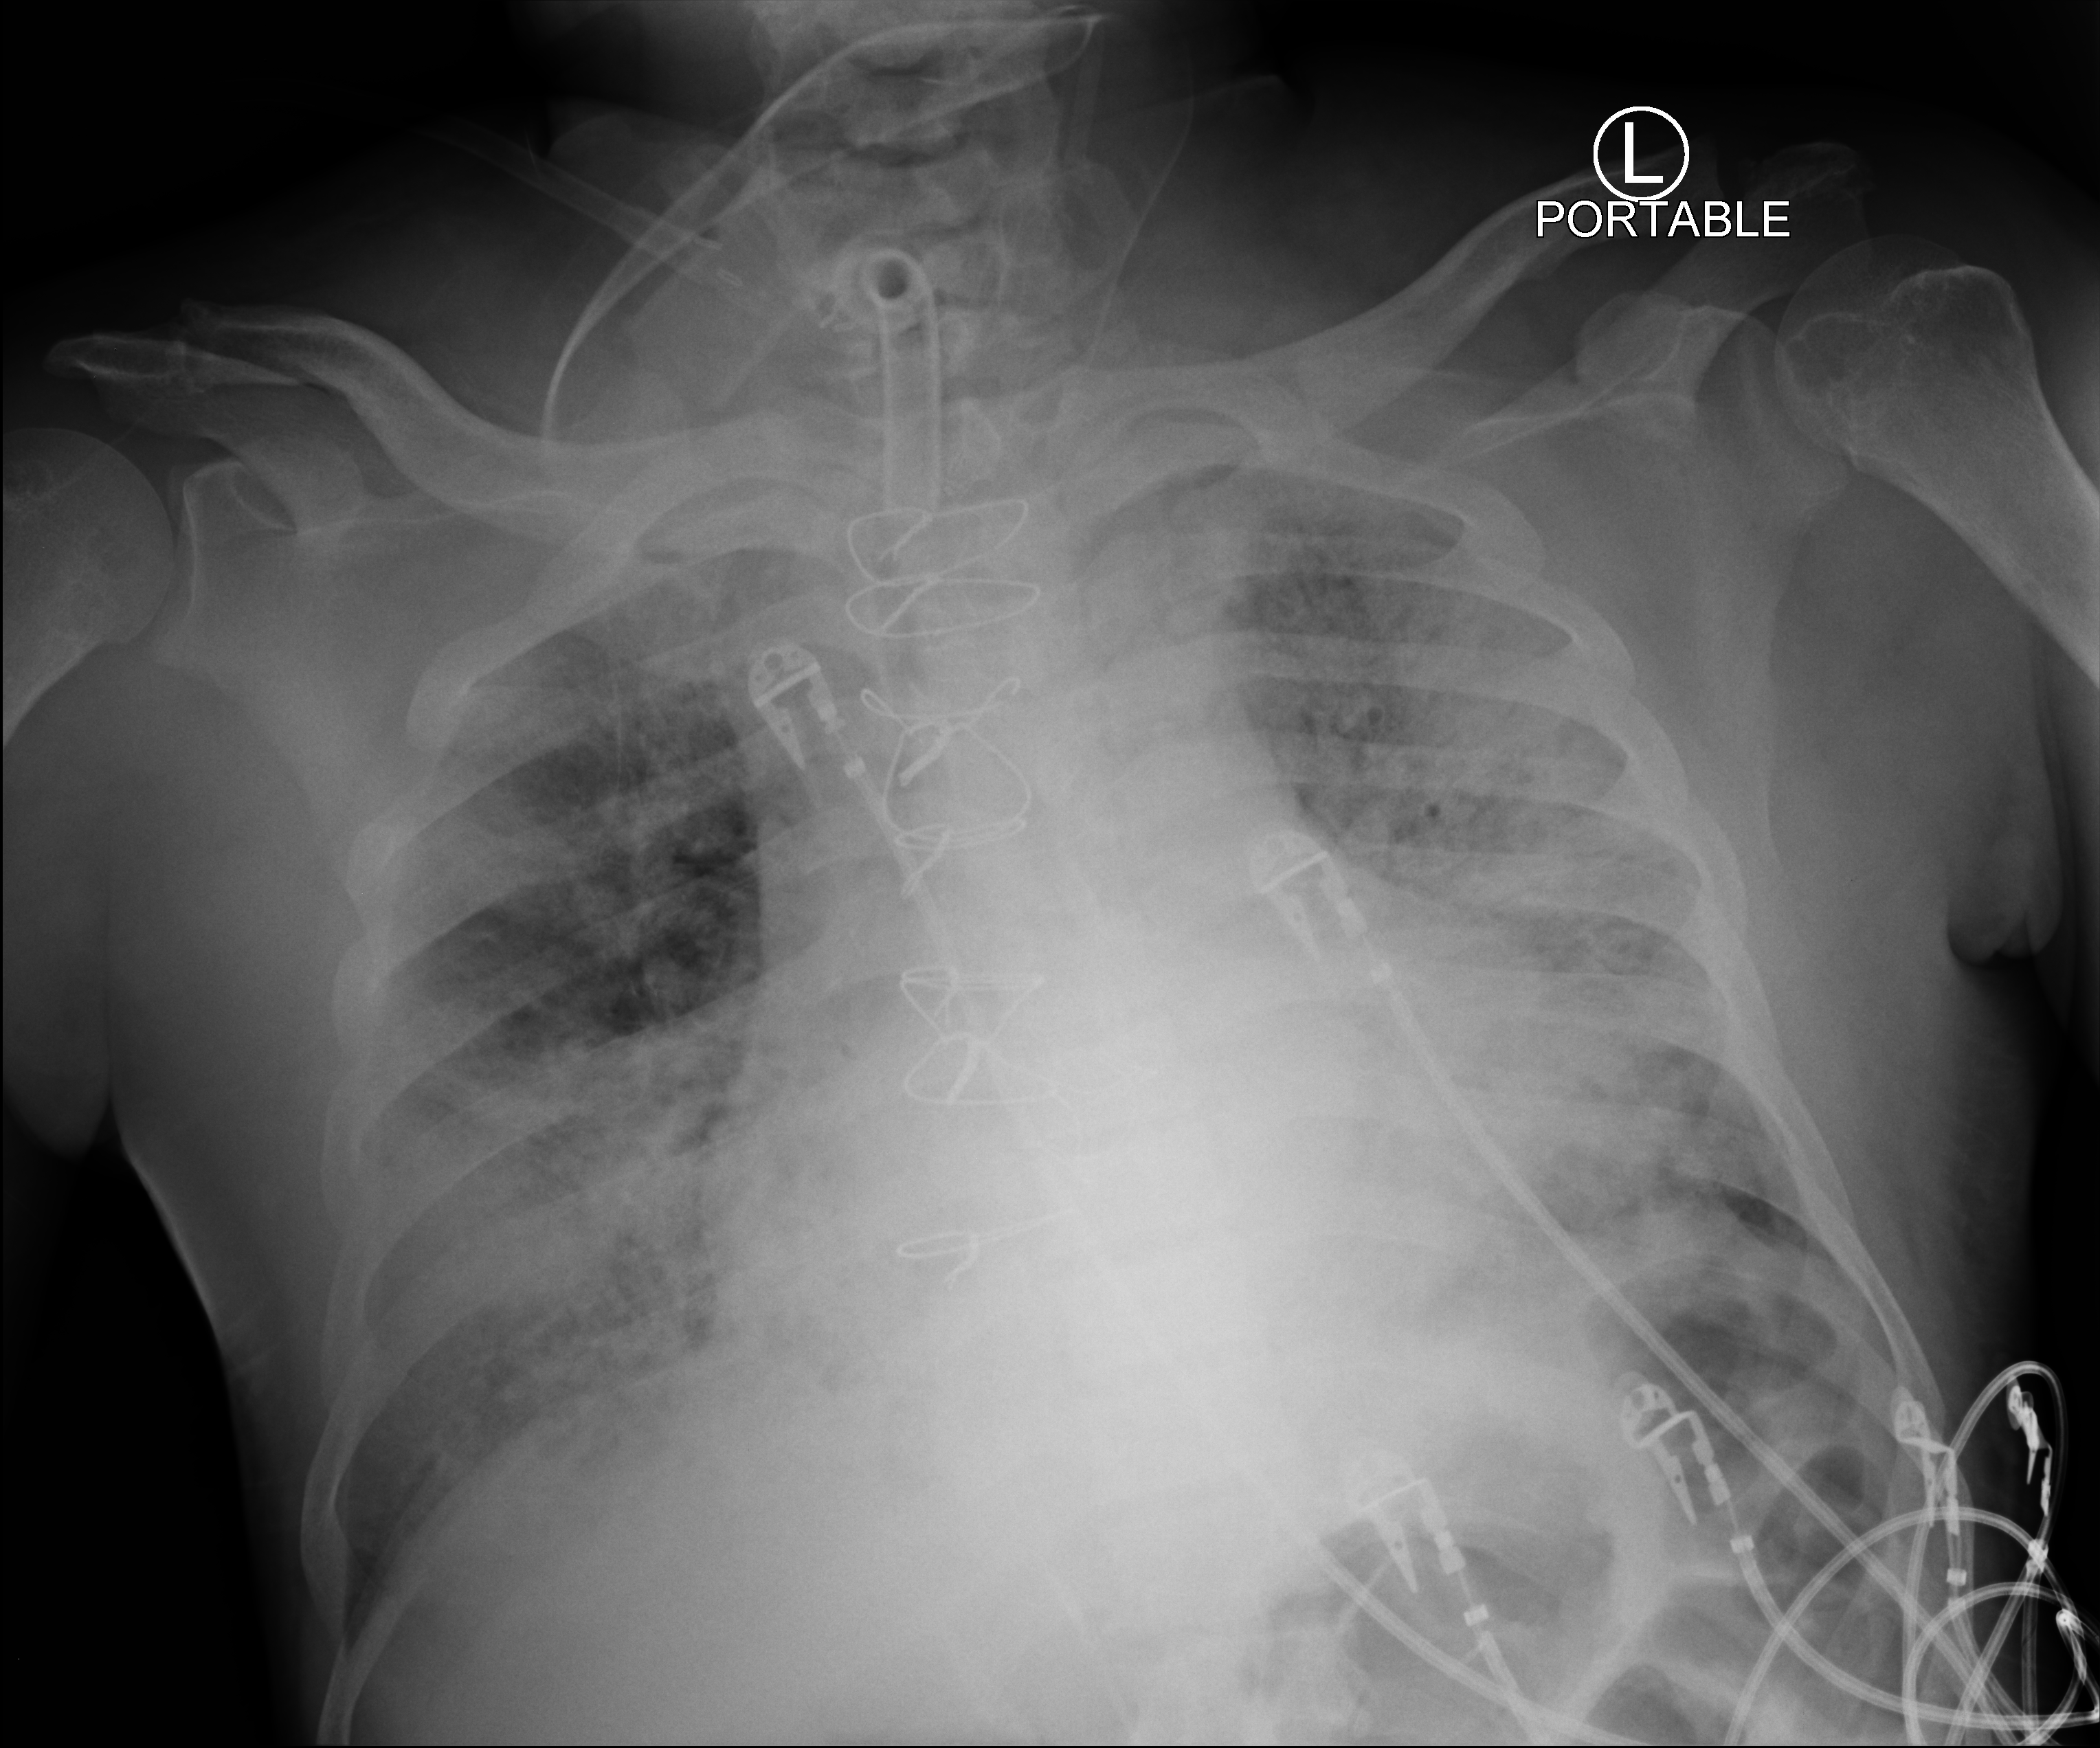
Chest X-ray (portable); anteroposterior (AP) projection. Patient hospitalised with COVID-19; male, aged 60–74 years.
From the hospital-stay record, not from the radiograph (when in the stay this image was taken is not recorded):
- admitted to intensive care during this hospital stay: yes
- mechanically ventilated during this hospital stay: yes
- COPD (admission record): no